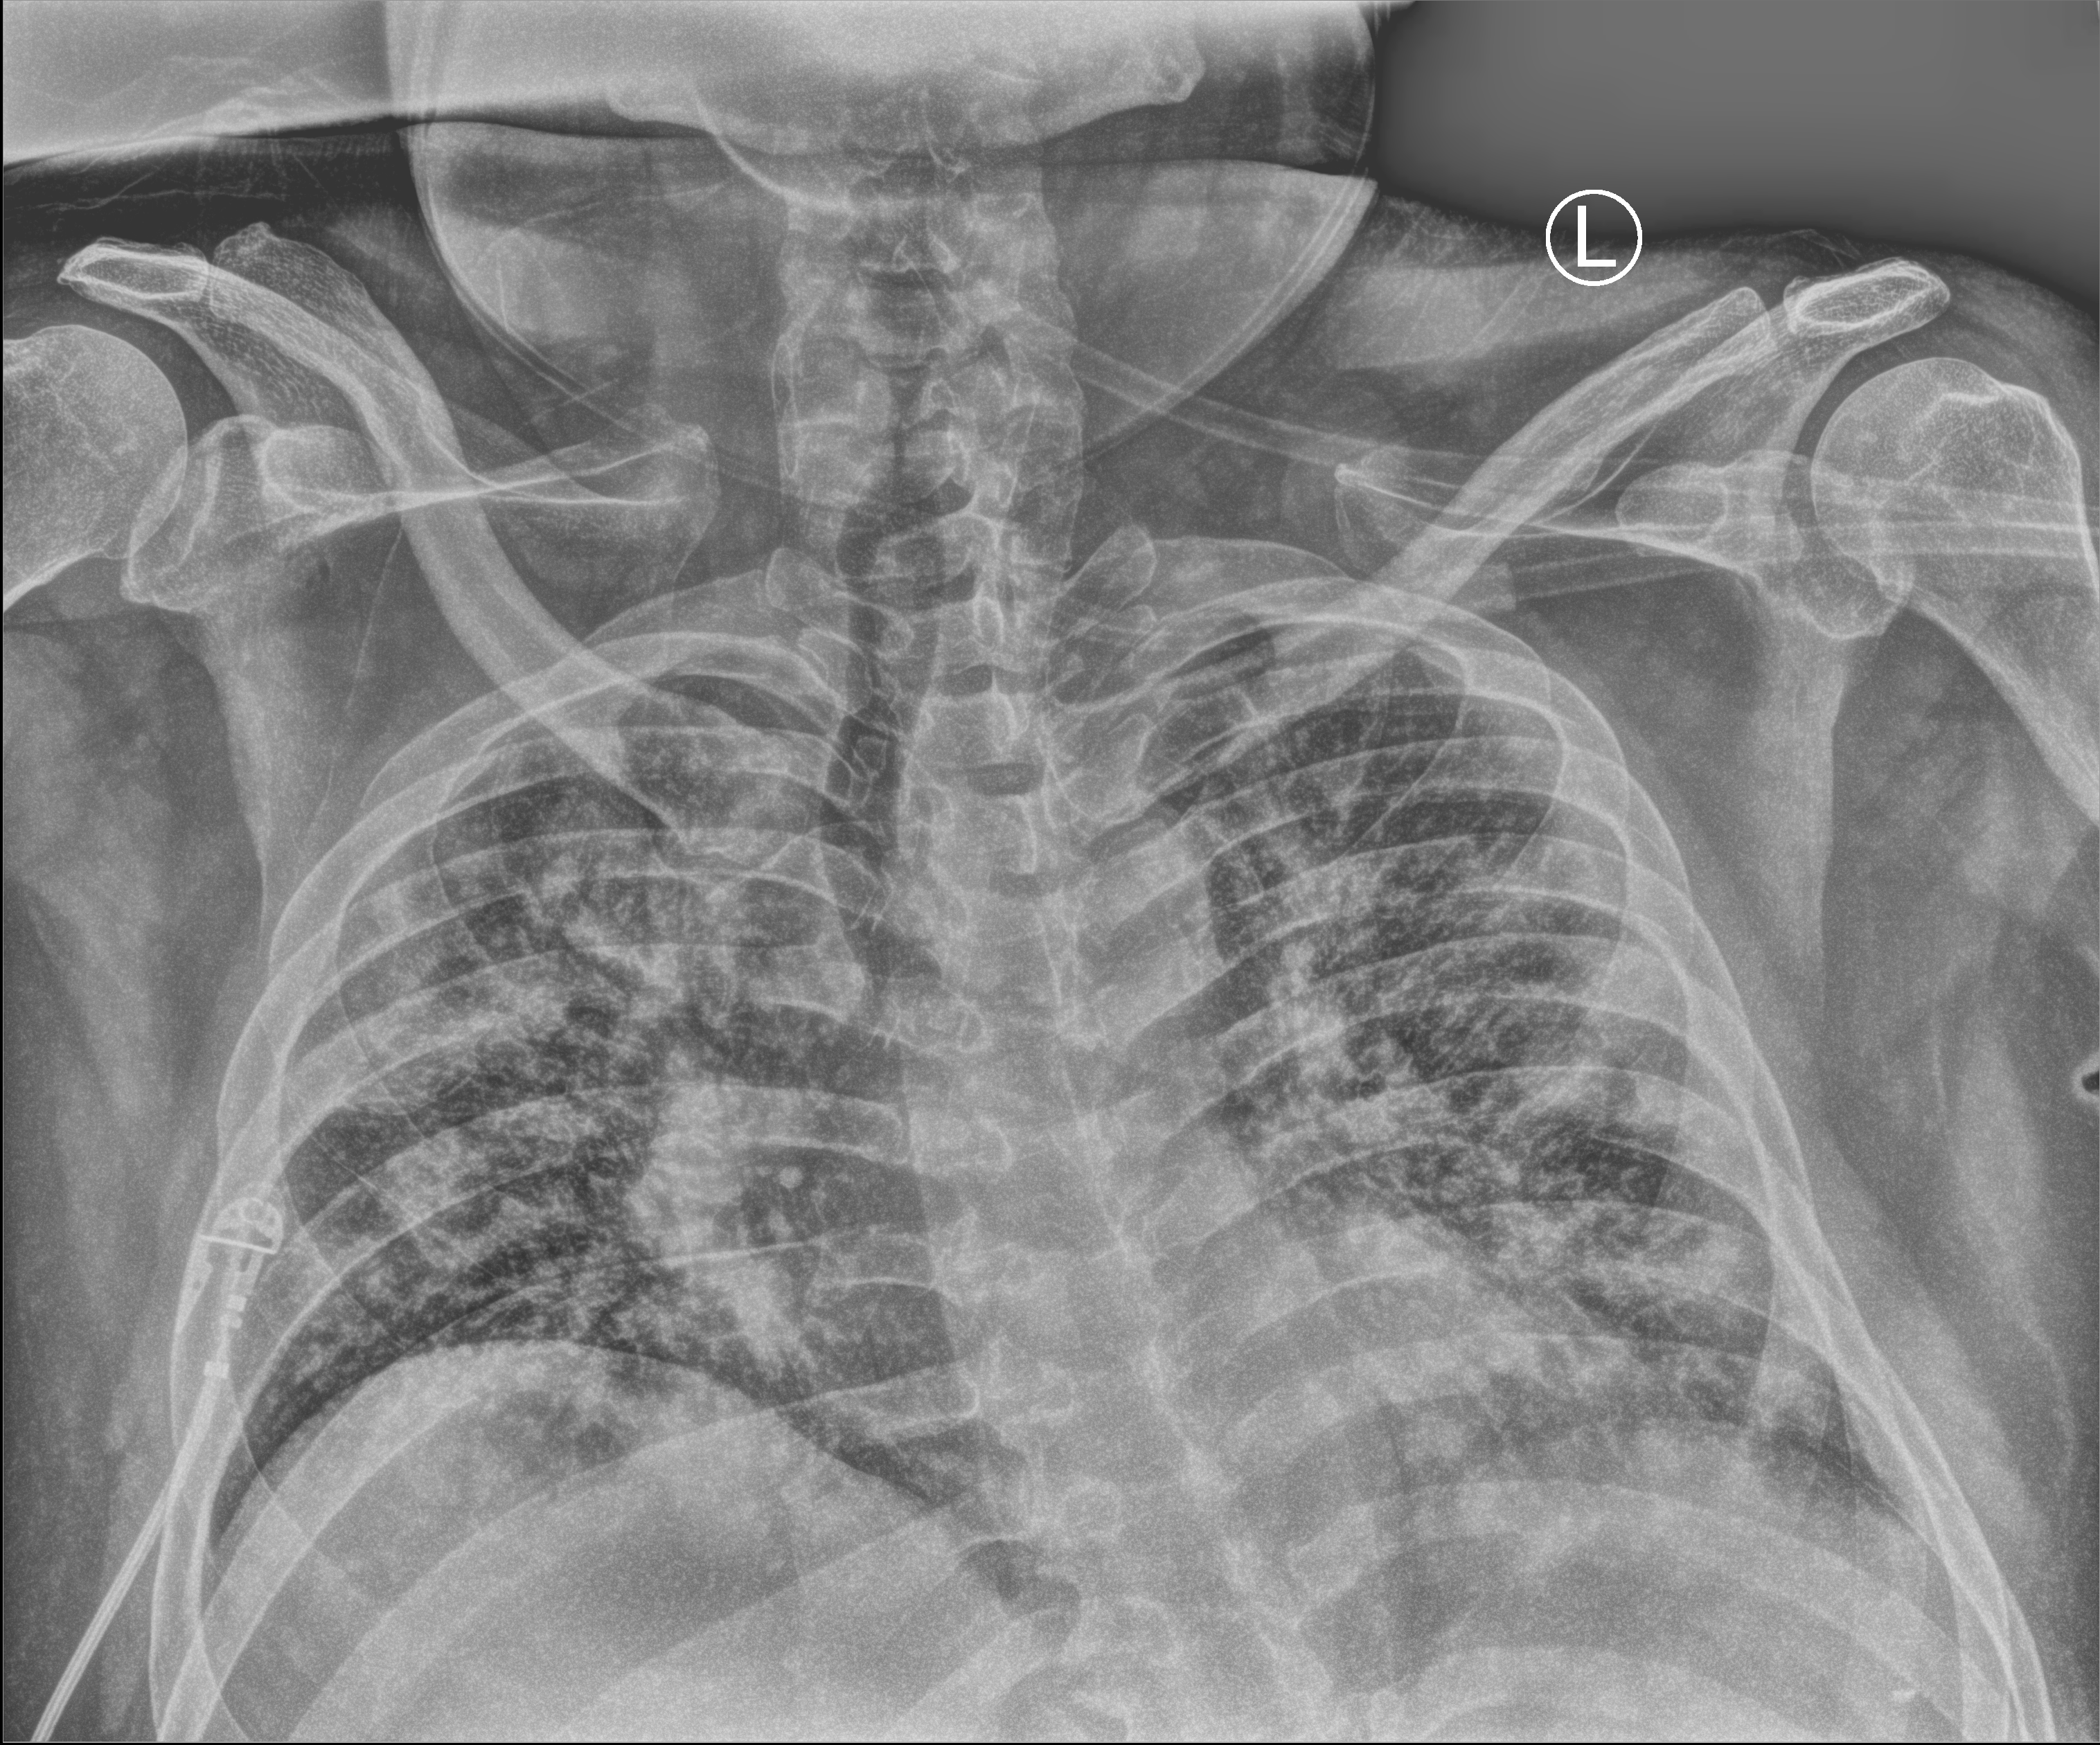
Chest X-ray (portable), anteroposterior (AP) projection. Male patient hospitalised with COVID-19, age 18–59 years.
Admission-level facts for this patient (not findings on this image; timing relative to this image not recorded): mechanically ventilated during this hospital stay: no.